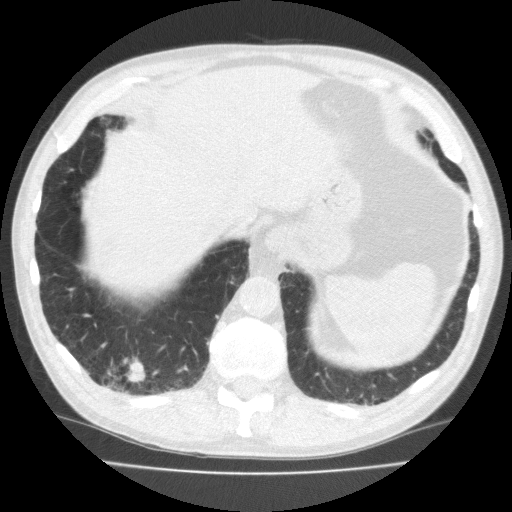
Low-dose screening chest CT, one axial slice. 120 kVp. Lung window (W 1500 / L -600 HU). 512 × 512 image matrix, field of view 350 × 350 mm.
Annotated regions visible in this slice (manually delineated by an expert):
- lesion 1 (tumor, lower lobe of right lung): bounding box (x1, y1, x2, y2) in pixels: (125, 358, 146, 385)